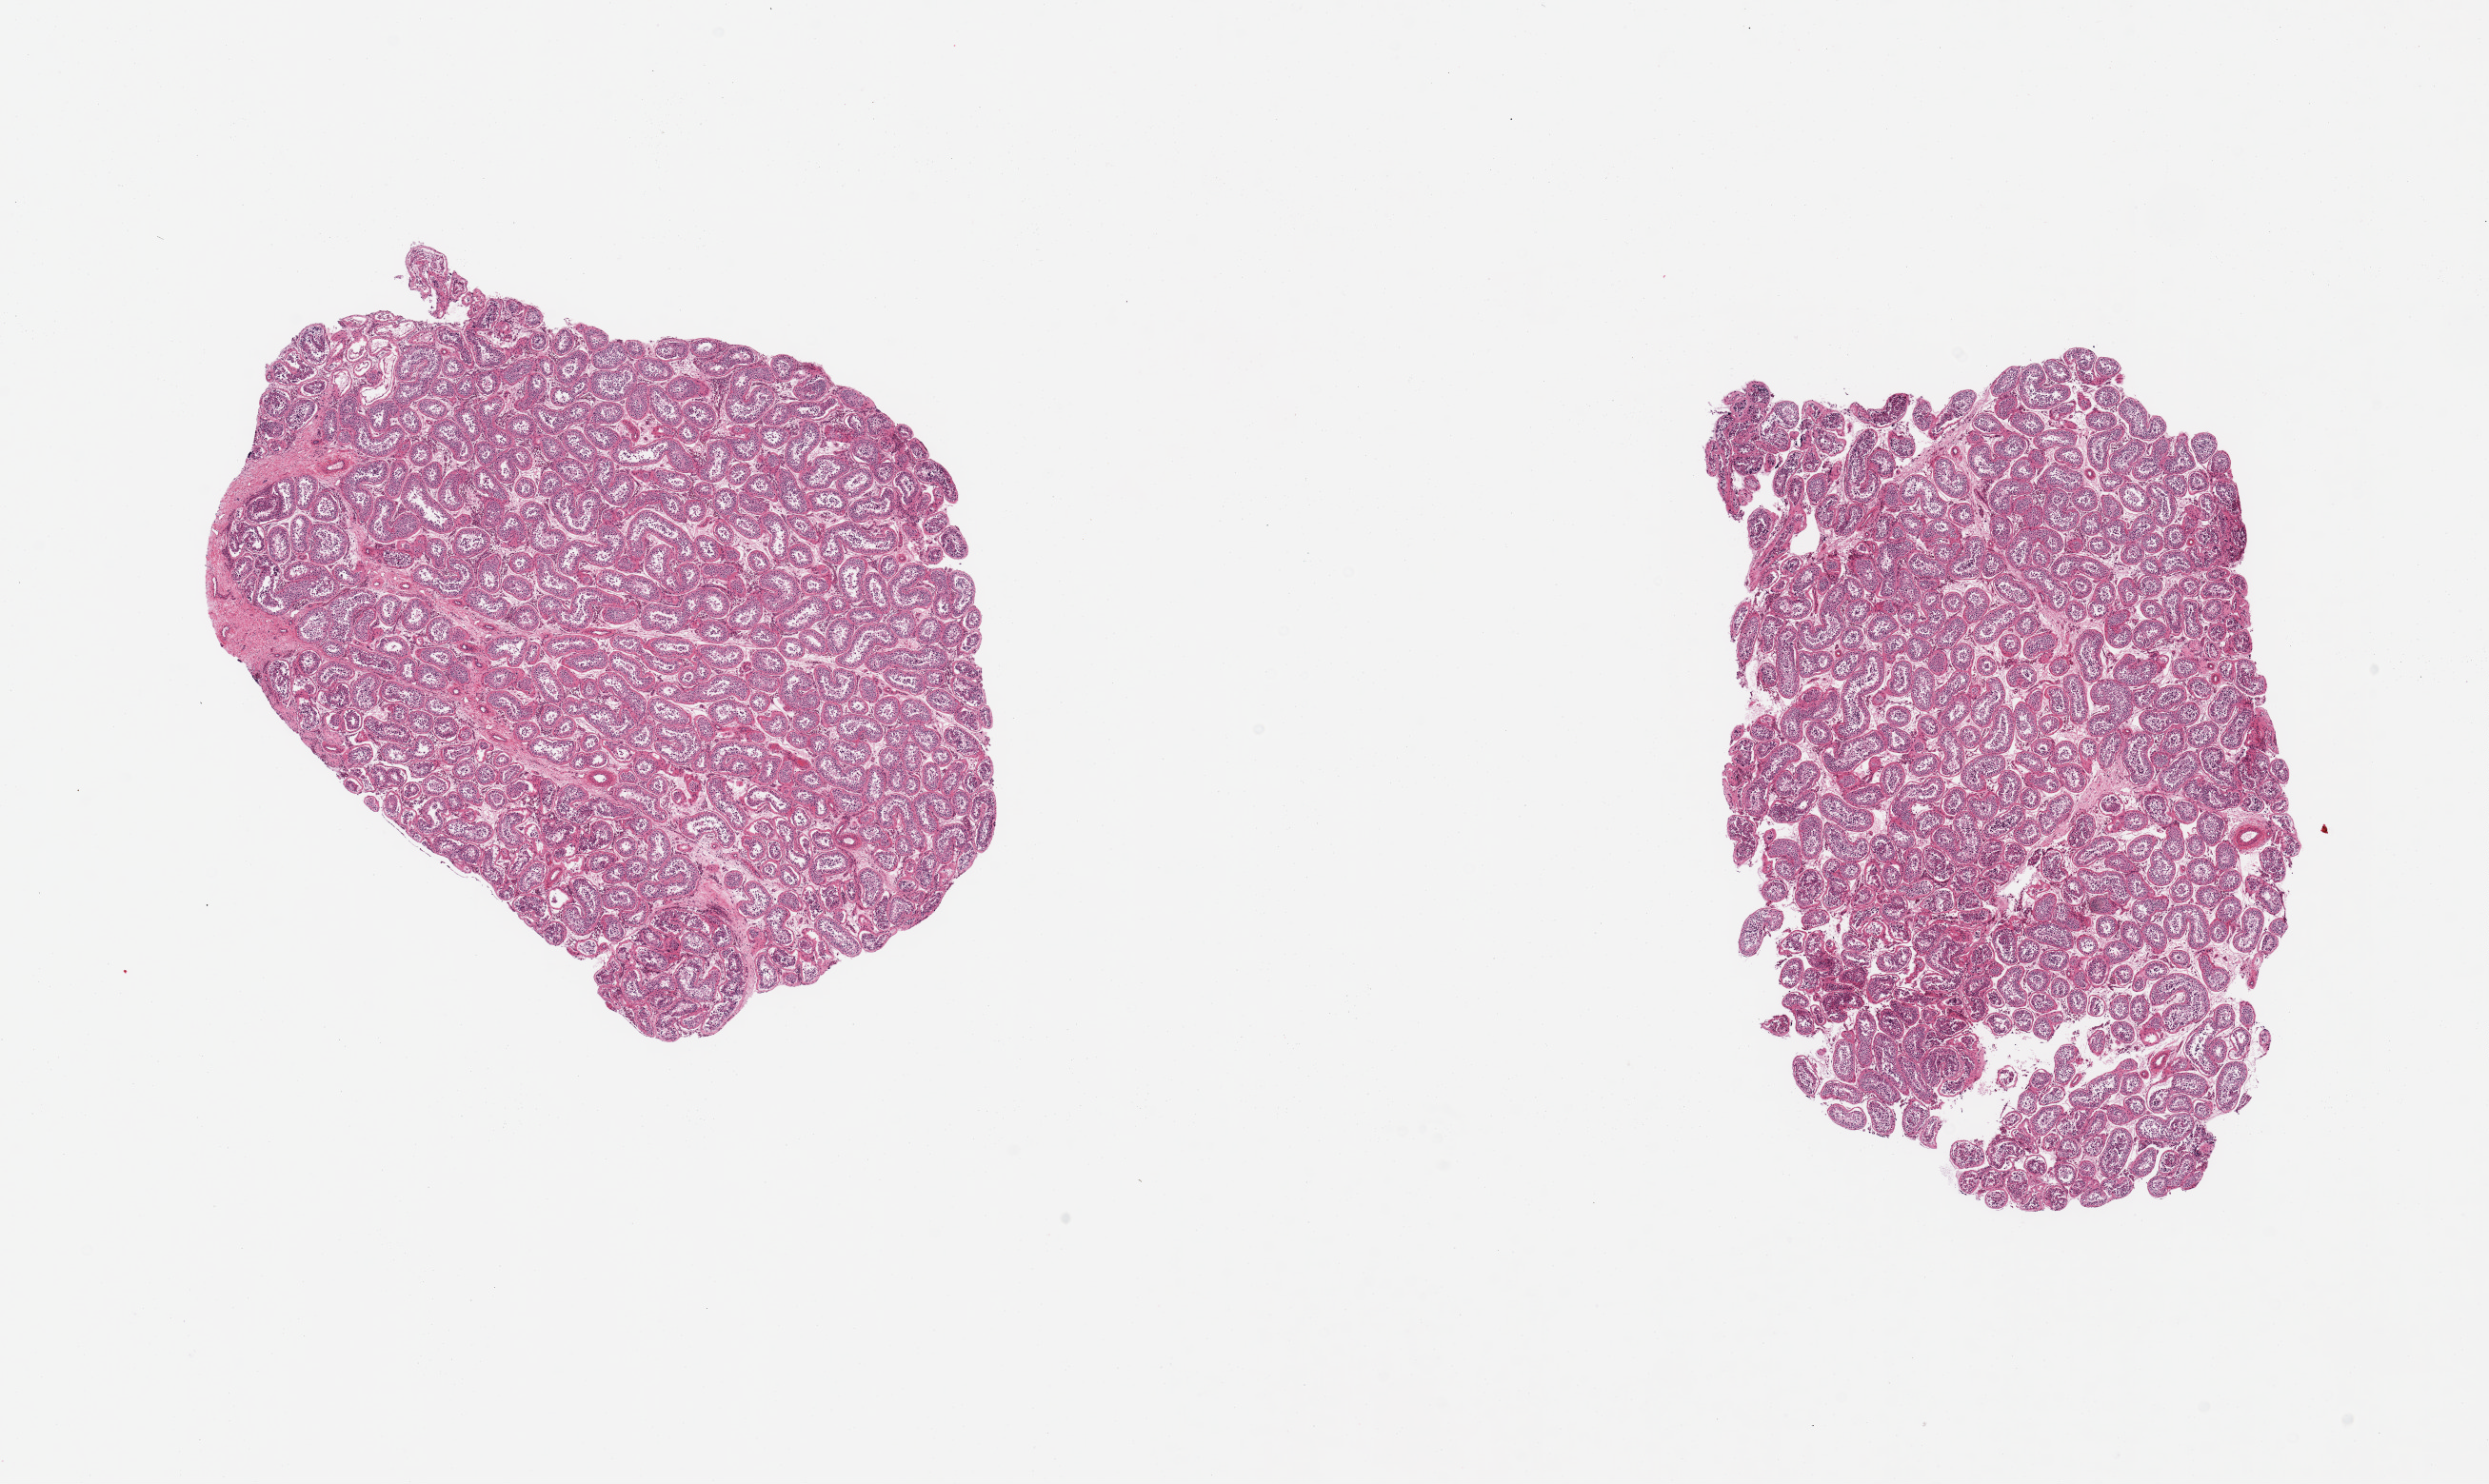
Haematoxylin and eosin whole-slide image, brightfield, a low-resolution overview of the entire scanned area, about 20.7 x 12.3 mm; PAXgene-fixed paraffin-embedded (PFPE) section; target tissue: testis; donor tissue sample. Donor sex: male.
* pathologist's review note for this sample: 2 pieces, markedly reduced spermatogenesis